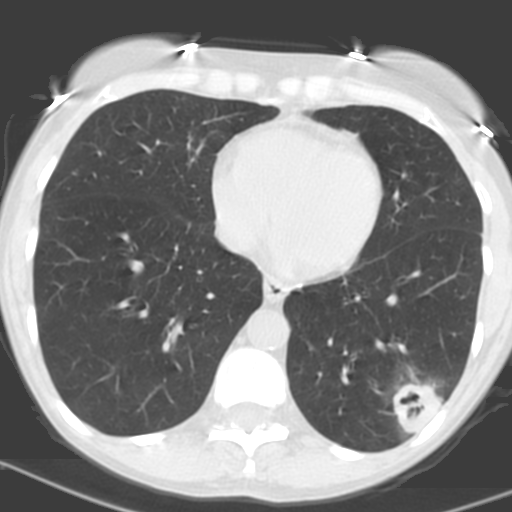
Low-dose screening chest CT, axial slice. Baseline screening round. Lung window (W 1500 / L -600 HU). 3.2 mm slice thickness. 120 kVp. 512 × 512 image matrix, field of view 262 × 262 mm. Female participant, aged 56 years at enrolment. Current smoker at enrolment.
- Expert-annotated lung lesion, bounding box (x1, y1, x2, y2) in pixels: (374, 364, 455, 436).
- Reader record for this screening exam (exam-level; its link to the box is not recorded): non-calcified nodule or mass ≥4 mm, left lower lobe, 31 × 23 mm, poorly defined margins, soft tissue attenuation, pre-existing on the prior screen: no.
- Official screen result: positive, change unspecified: nodule(s) >= 4 mm or enlarging nodule(s), mass(es), or other non-specific abnormalities suspicious for lung cancer.
- Participant outcome: lung cancer diagnosed 27 days after this screen — squamous cell carcinoma, NOS, left lower lobe, poorly differentiated (G3), stage IB (AJCC 6th edition), 35 mm at pathology.